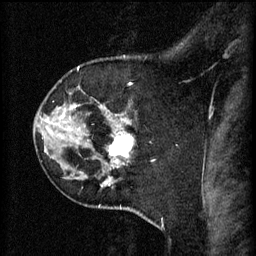
Breast MRI (dynamic contrast-enhanced), one sagittal slice; slice 48 of 60 in the series (ordered by position); 3 images stored at this slice position (order not interpretable as contrast timing); 1.5 T; TE 4.2 ms, TR 11 ms; 256 × 256 image matrix, field of view 180 × 180 mm. Female patient, age 45 years.
Structures marked on this image (semi-automatically segmented with operator editing):
- analysis volume of interest (the breast-tissue region the enhancement analysis was run in; not a lesion): bounding box (x1, y1, x2, y2) in pixels: (102, 128, 135, 171)
- tumour enhancement mask (voxels above the 70 % enhancement threshold inside the analysis volume of interest): (108, 134, 135, 163)